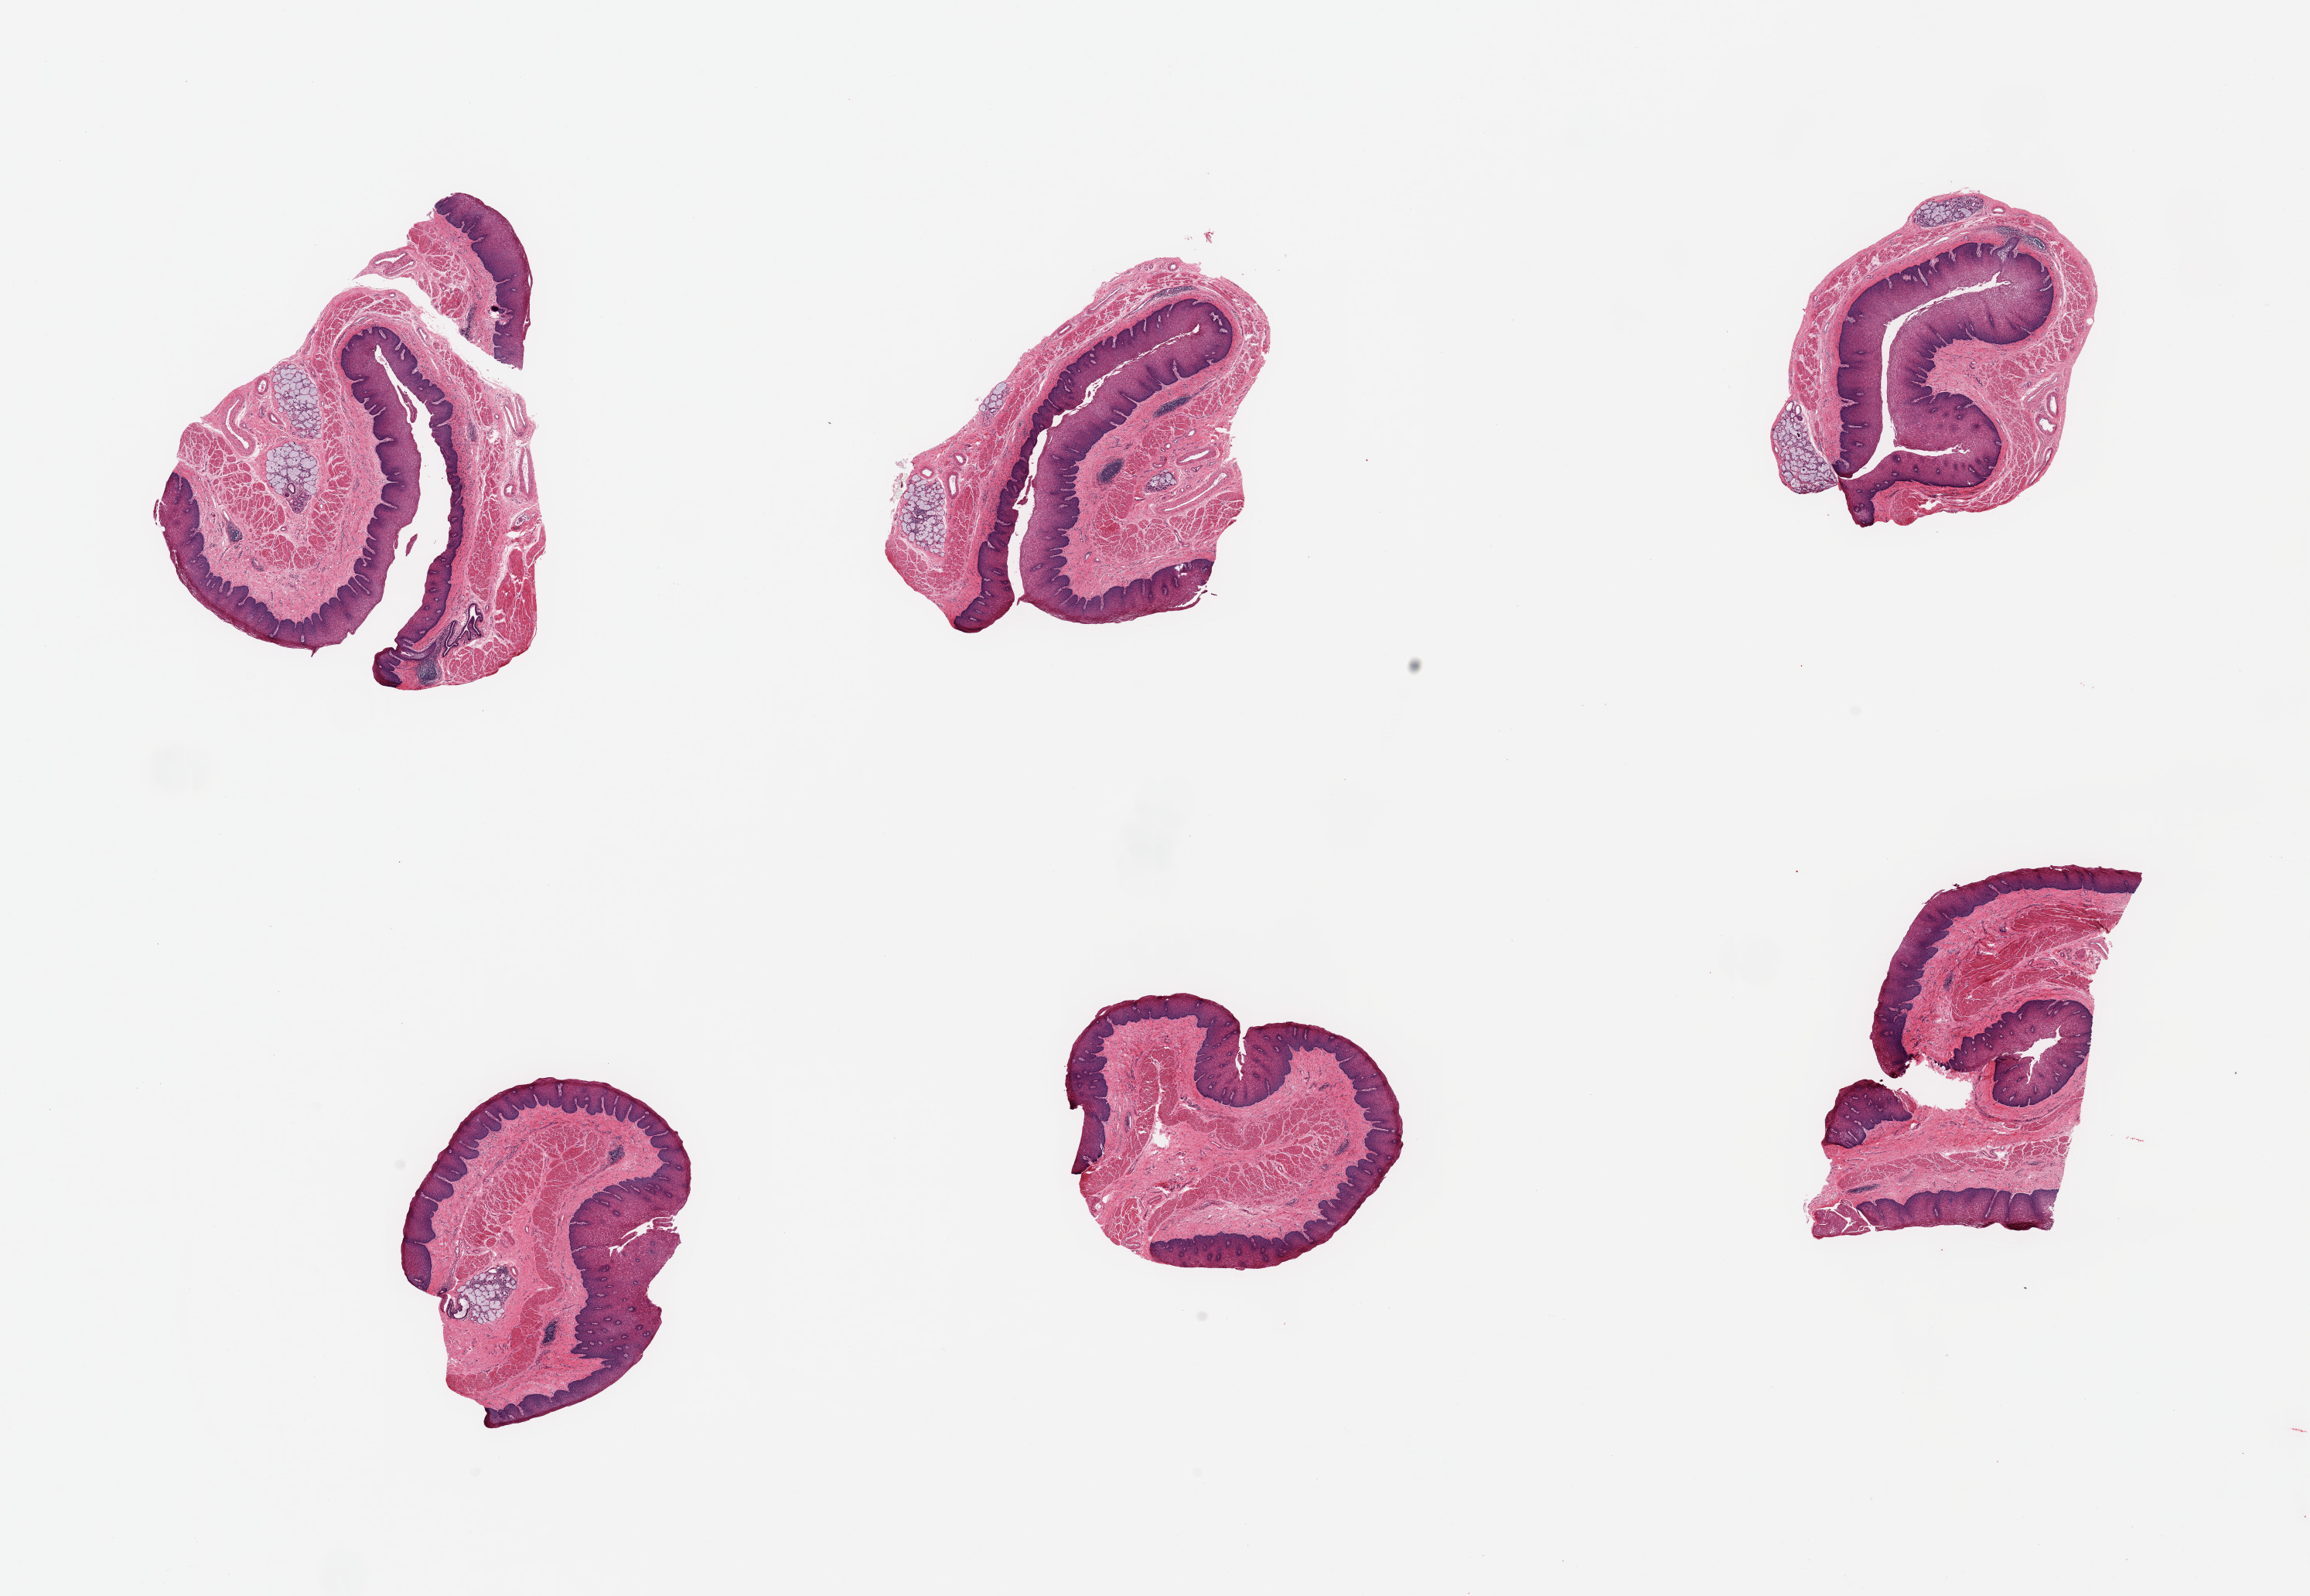
H&E whole-slide image, brightfield, shown as a low-resolution overview of the whole scanned area (about 23.6 x 16.3 mm, slide scanned at 20x); PAXgene-fixed paraffin-embedded (PFPE) section; target tissue: esophageal mucous membrane; donor tissue sample.
Review note (as recorded): 6 pieces; well preserved mucosa; 4 pieces contain submucosal mucous glands up to 10%.